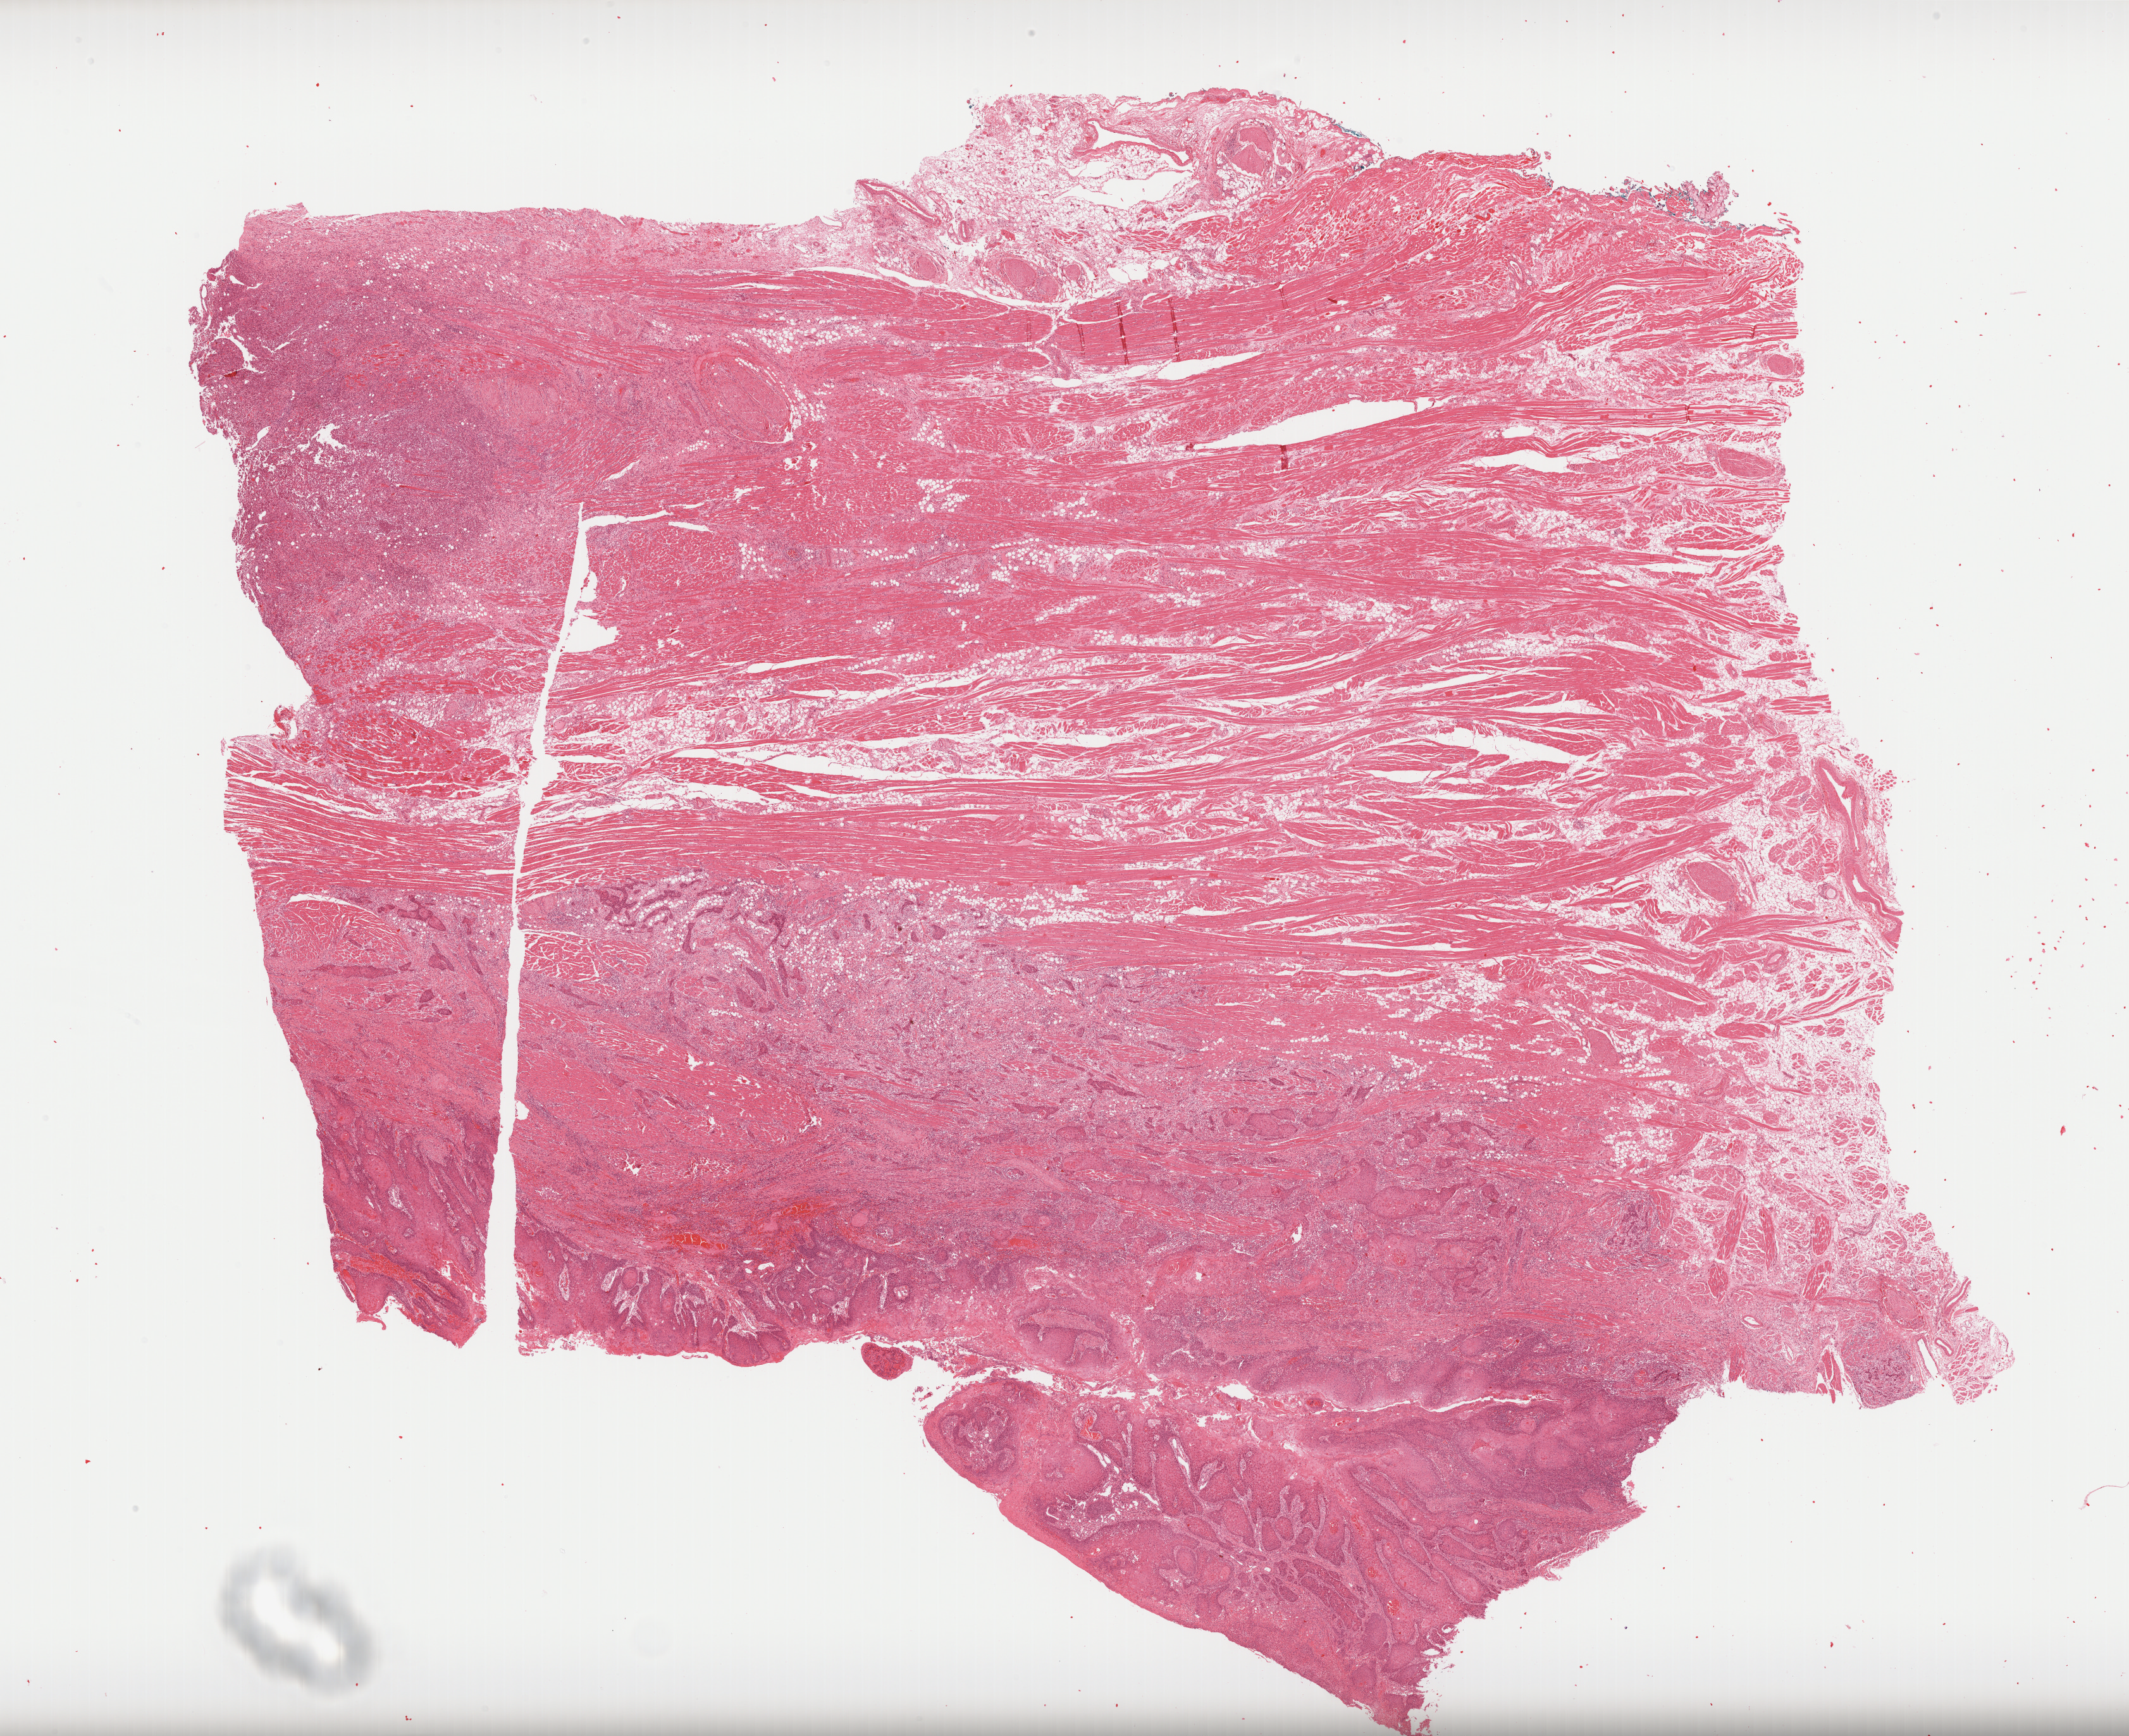
H&E whole-slide image, a low-resolution overview of the entire scanned area, about 27.1 x 22.1 mm. Formalin-fixed paraffin-embedded (FFPE) diagnostic section. Primary tumour sample from the head and neck. Female, age 50 years at initial diagnosis. Histologic grade: G2 (moderately differentiated).
Lymph nodes positive (case pathology): 1 of 55 examined. Histologic diagnosis: Squamous cell carcinoma, NOS (tongue, NOS). AJCC pathologic stage: IVA. Laterality: right.